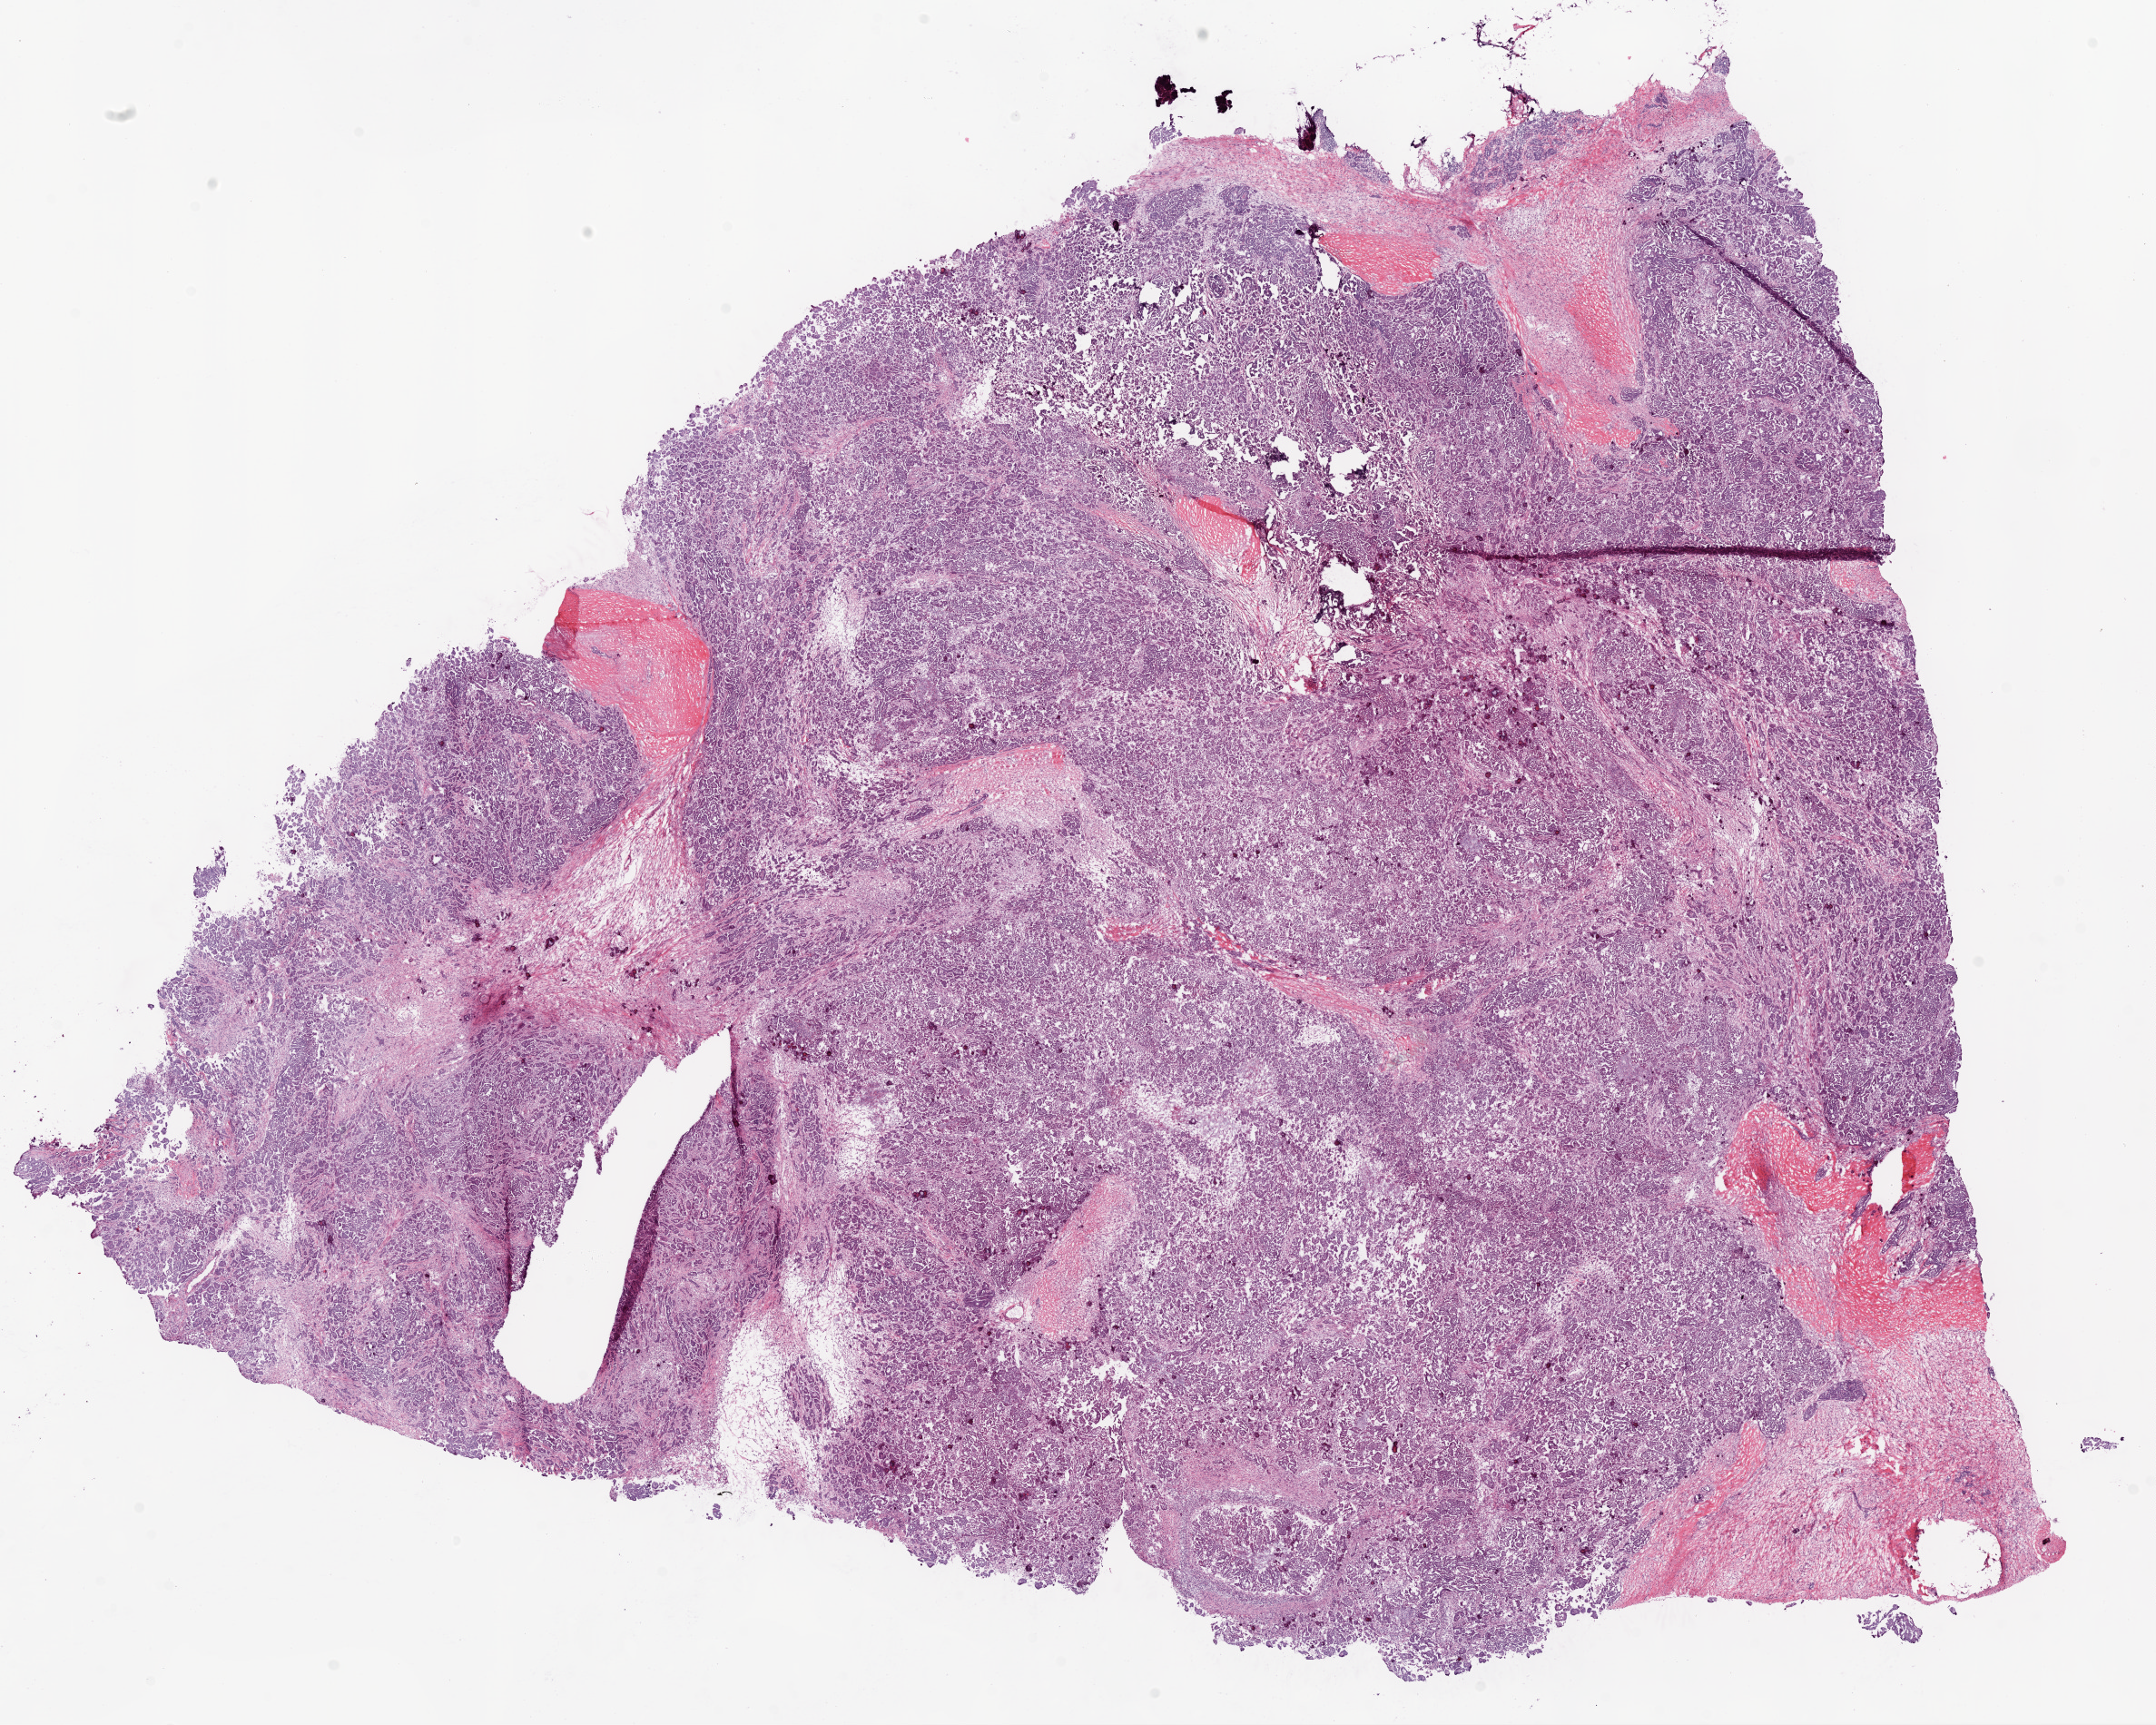
Whole-slide histology image, H&E-stained, low-resolution overview of the scanned area, about 19.1 x 15.2 mm (acquisition: 20x scan), frozen section from the bottom of the tissue portion, ovary, primary tumour sample. Female patient; age at initial diagnosis 36 years. Composition of this section per pathologist review: tumour cells 90%, tumour nuclei 95%.
Diagnosis: Serous cystadenocarcinoma, NOS.